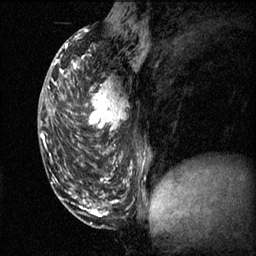
Breast MRI (dynamic contrast-enhanced), one sagittal slice; position 27 of 60 along the scan axis; 3 images stored at this slice position (order not interpretable as contrast timing); 1.5 T; TE 4.2 ms, TR 11.1 ms; 2 mm slice thickness; 256 × 256 image matrix, field of view 180 × 180 mm. Patient: female, 50 years.
Outlined on this slice (semi-automatically segmented with operator editing):
- analysis volume of interest (the breast-tissue region the enhancement analysis was run in; not a lesion): bounding box <68,68,137,141> (left, top, right, bottom; pixels)
- tumour enhancement mask (voxels above the 70 % enhancement threshold inside the analysis volume of interest): <75,68,128,137>